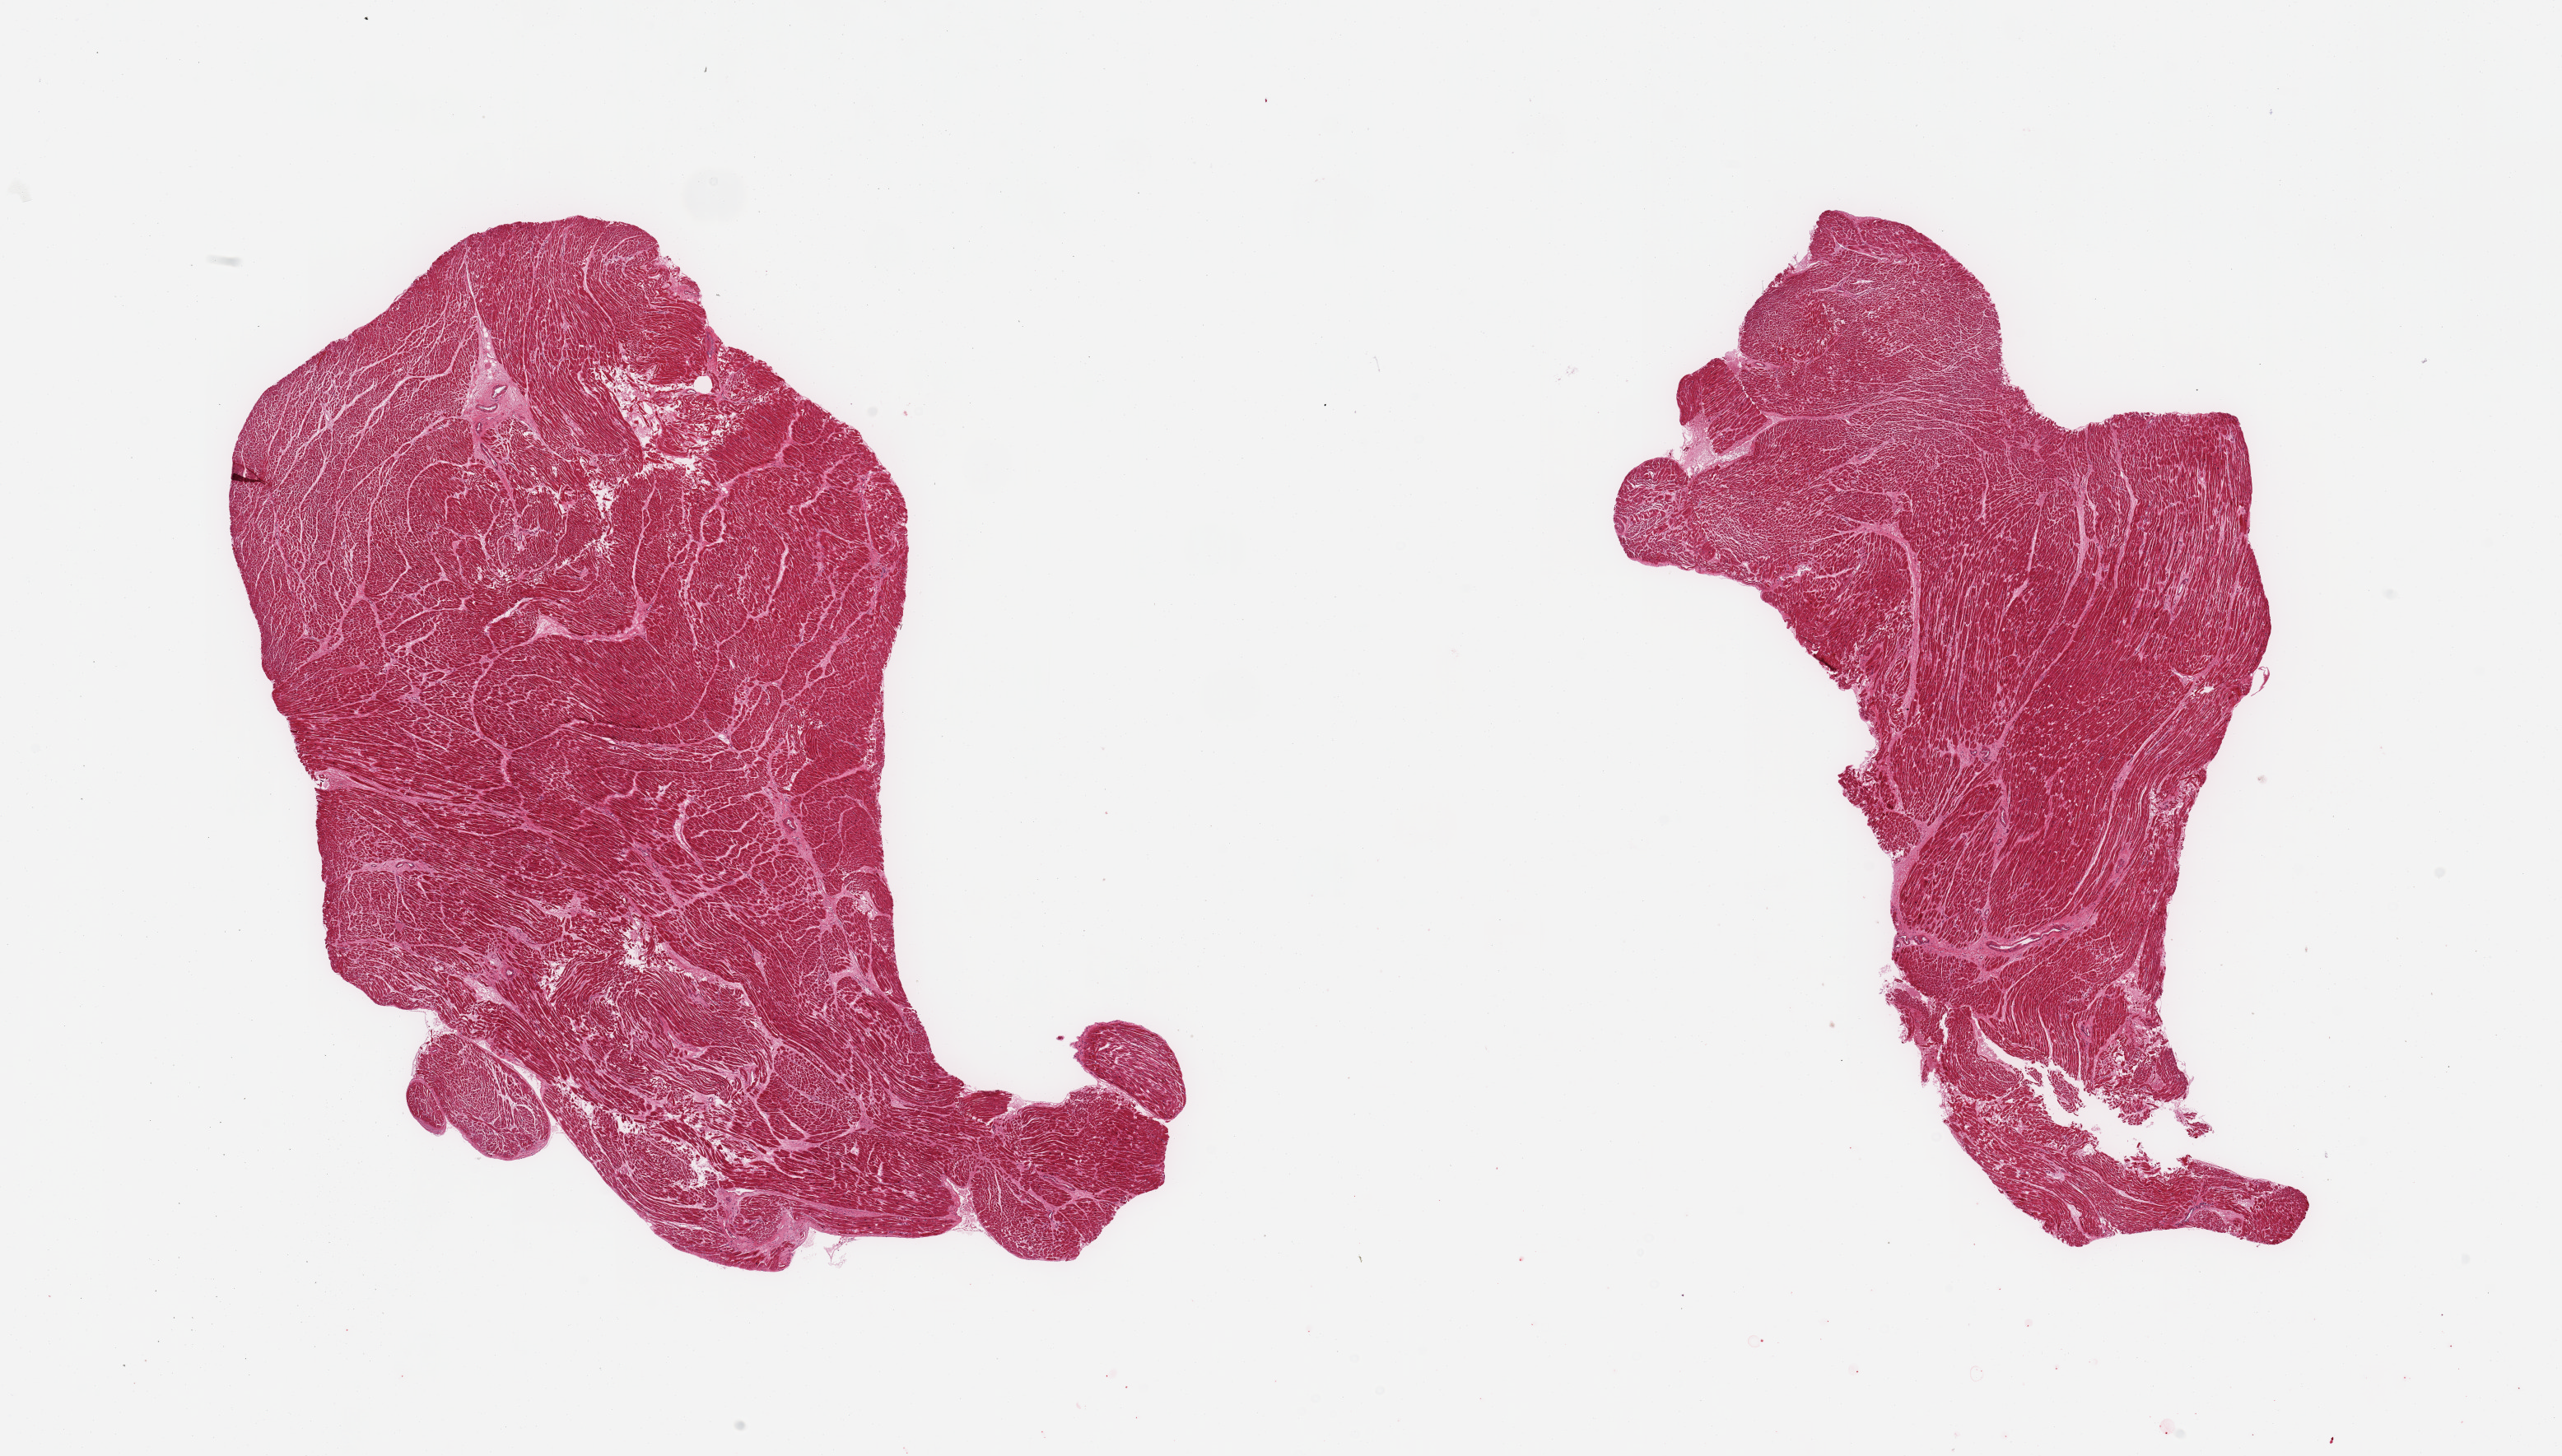
Digitized H&E-stained section, shown as a low-resolution overview of the whole scanned area (about 24.6 x 14.0 mm, acquisition: 20x scan), PAXgene-fixed, paraffin-embedded tissue, sampled site (target tissue): heart, tissue donor sample.
* review note (as recorded): 2 pieces; mild increase in interstitial fibrous tissue